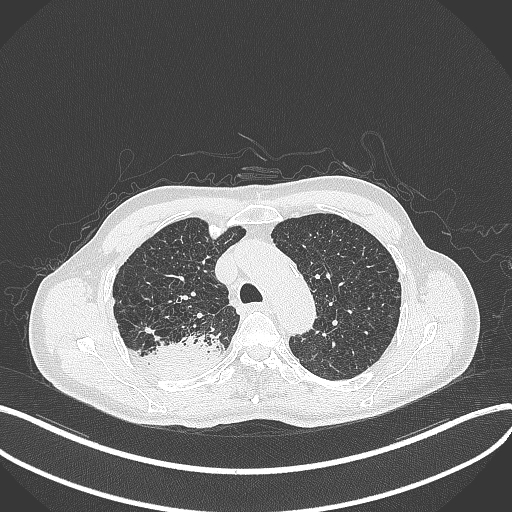
Chest CT, one axial slice. Position 333 of 428 along the scan axis. 120 kVp. Lung window (W 1500 / L -600 HU). 512 × 512 image matrix. Male patient, age 79 years. From the clinical record (not read from this slice): clinical TNM (as recorded): T3 N0 M0.
Annotated regions visible in this slice (bounding box drawn by a radiologist):
- lung tumour (recorded histology: adenocarcinoma): bounding box (x1, y1, x2, y2) in pixels: (146, 330, 226, 376)